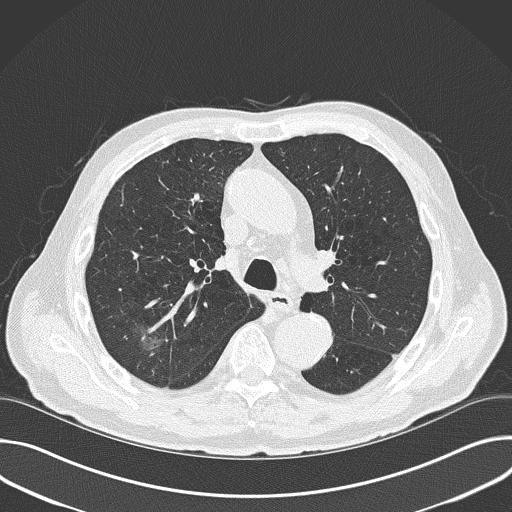
Low-dose screening chest CT, one axial slice. Slice 110 of 177 in the series (ordered by position). Reconstruction kernel B50f. Lung window (W 1500 / L -600 HU). 2 mm slice thickness. 512 × 512 image matrix.
Outlined on this slice (expert manual segmentation):
- lesion 1 (tumor, upper lobe of right lung): bounding box (x1, y1, x2, y2) in pixels: (139, 335, 162, 351)